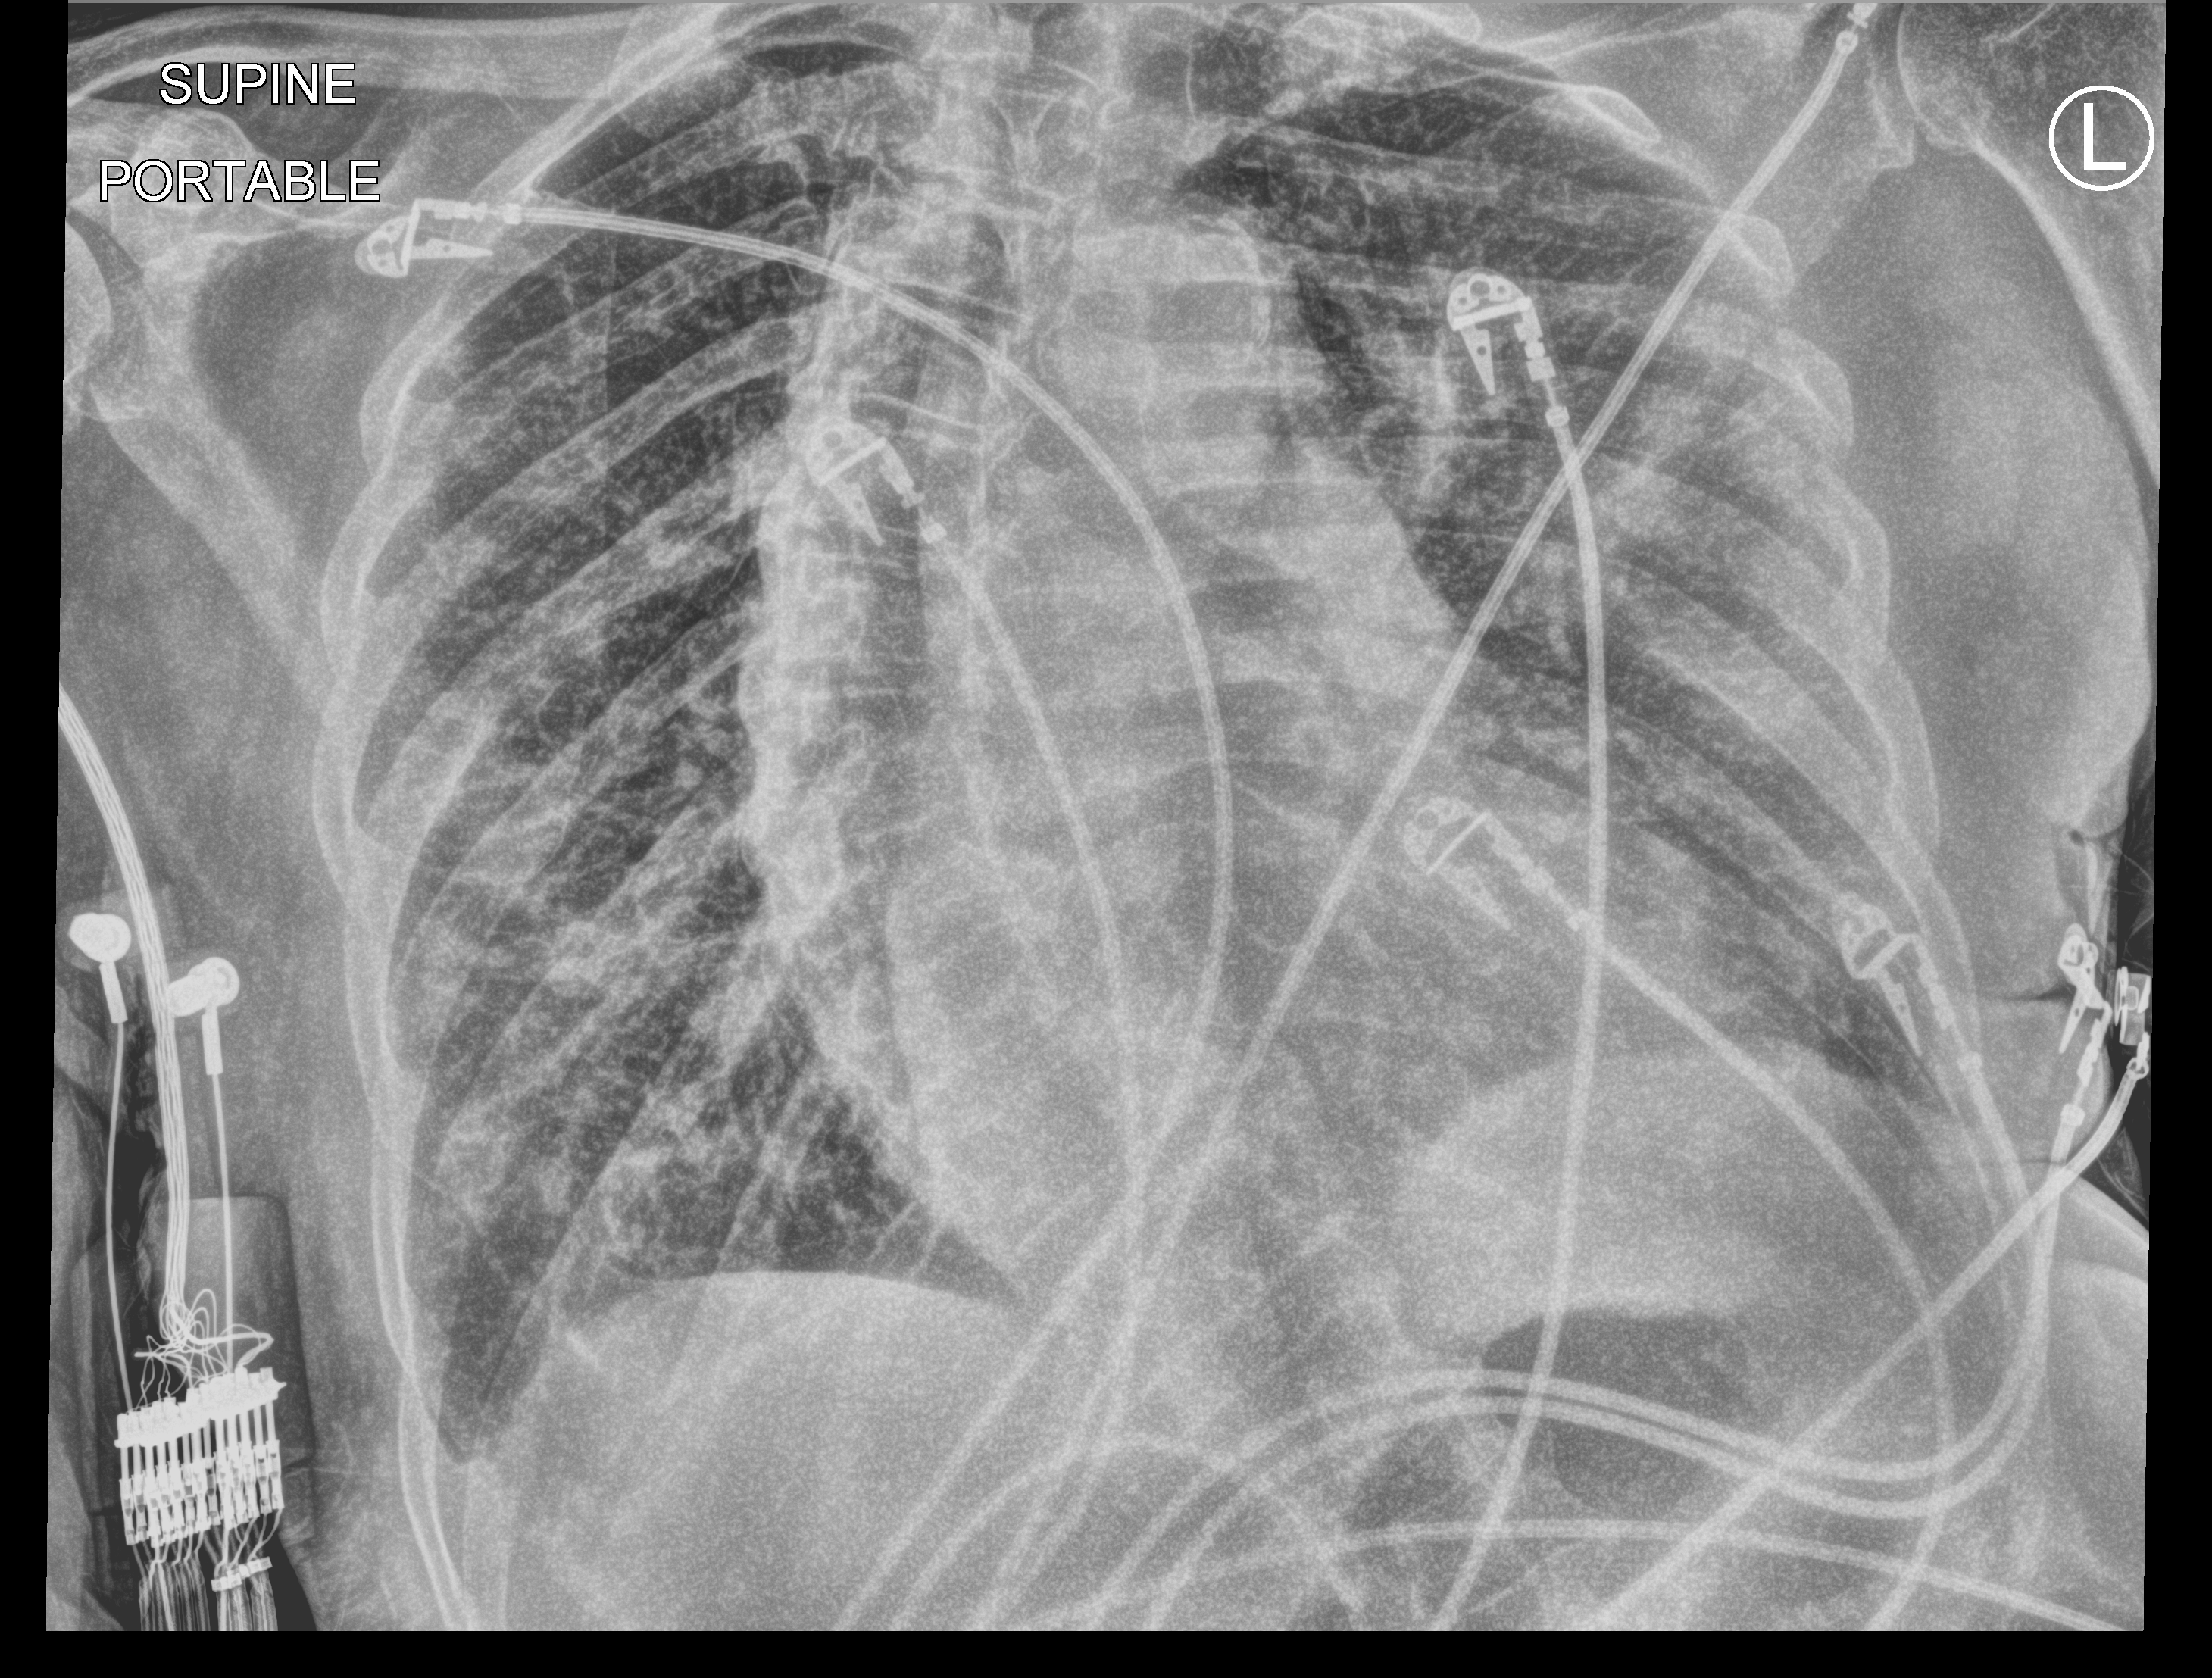
Bedside chest radiograph (computed radiography); anteroposterior (AP) projection. Patient hospitalised with COVID-19; male, aged 75–90 years.
Hospital-stay facts (about this admission, not read from this image; timing relative to this image not recorded): mechanically ventilated during this hospital stay: no; admitted to intensive care during this hospital stay: no.